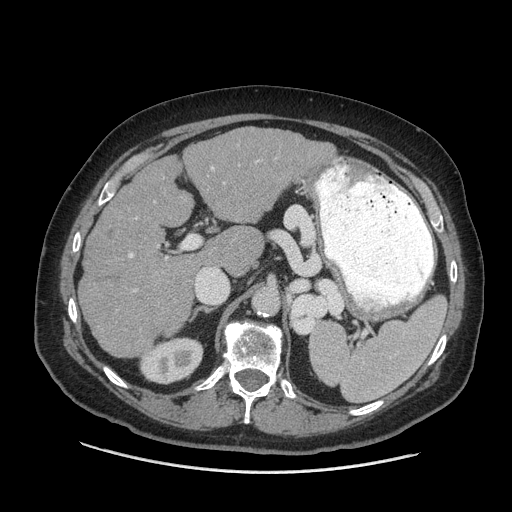
Contrast-enhanced abdominal CT (liver protocol), one axial slice; position 37 of 77 along the scan axis; reconstruction kernel STANDARD; 140 kVp; soft-tissue window (W 400 / L 40 HU); 2.5 mm slice thickness; 512 × 512 image matrix, field of view 420 × 420 mm. From the clinical record (not read from this slice): diagnosis: hepatocellular carcinoma (patient treated with transarterial chemoembolisation; whether this scan precedes or follows treatment is not stated here); TNM stage (as recorded): Stage-I; Child-Pugh class: A; tumour nodularity: uninodular; tumour size: 3.8 cm.
Outlined on this slice (semi-automatic segmentation, software-assisted and operator-edited):
- liver parenchyma outside the tumour (the mass and vessels are separate outlines, so this box may not span the whole liver): bounding box (x1, y1, x2, y2) in pixels: (78, 126, 336, 358)
- liver vessels: (128, 167, 214, 259)